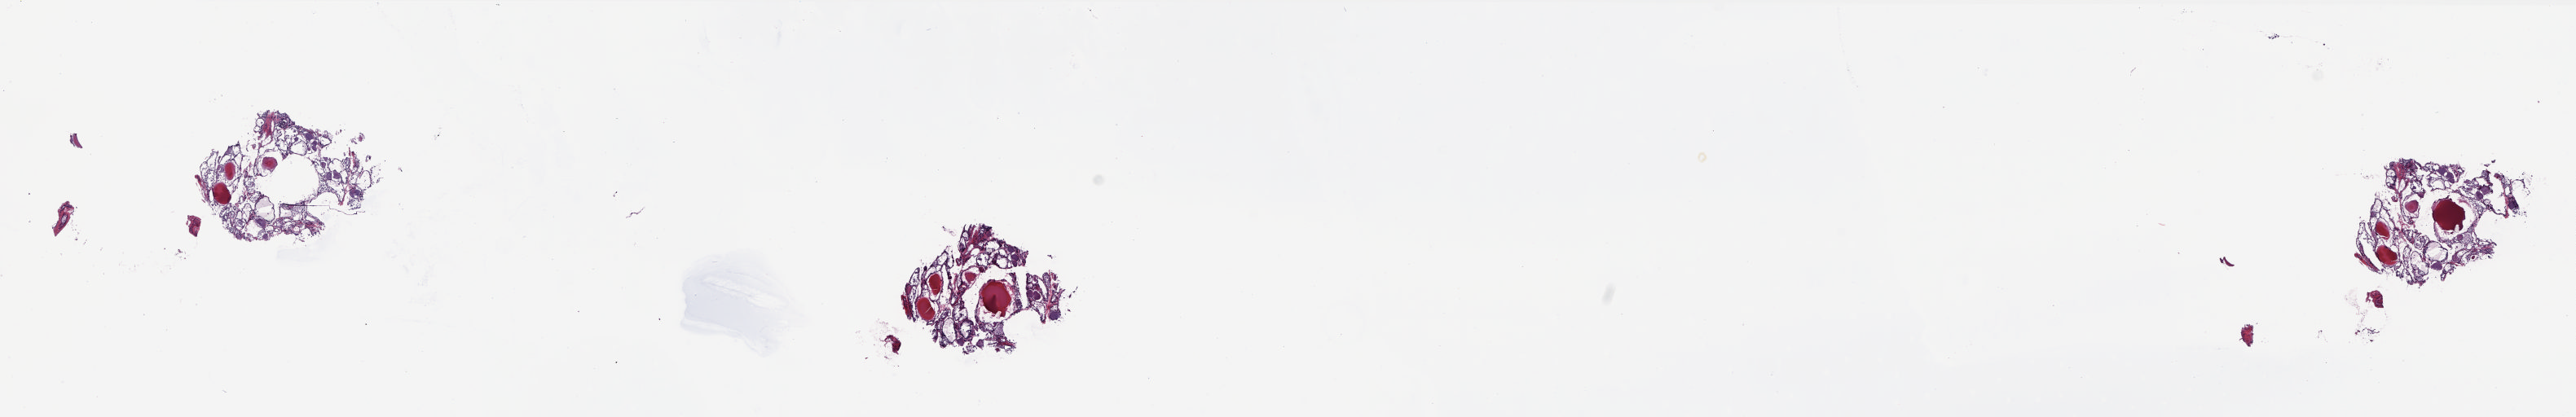
Whole-slide histology image, H&E — whole scanned area (about 25.5 x 4.1 mm, acquisition: 20x scan) shown as a low-resolution overview. Frozen section. Solid tissue normal (non-tumour tissue) sample from the thyroid. Male patient; age at initial diagnosis 74 years. Pathologist review of this section (percent, as recorded): tumour cells 0%, tumour nuclei 0%, normal cells 100%, stromal cells 0%, necrosis 0%. Inflammatory infiltration, as recorded: lymphocyte infiltration 2%, monocyte infiltration 5%, neutrophil infiltration 0%.
This section: solid tissue normal (non-tumour) sample from the same patient. Patient diagnosis: Papillary adenocarcinoma, NOS (thyroid gland).